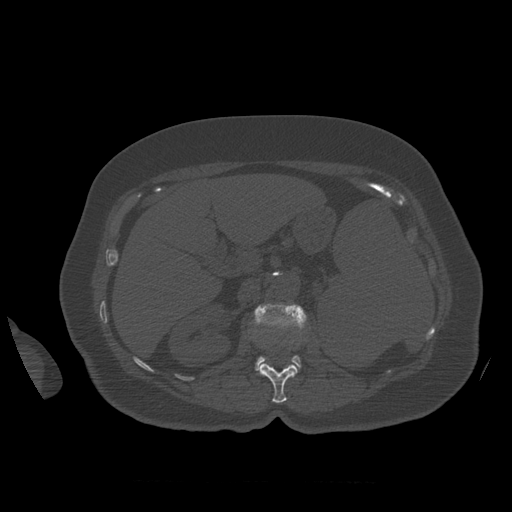
CT including the spine, one axial slice. Position 268 of 399 along the scan axis. Reconstruction kernel STANDARD. Bone window (W 1800 / L 400 HU). 1.25 mm slice thickness. 512 × 512 image matrix. Patient age 81 years. Case-level facts recorded for this patient, not image findings: primary cancer: renal; vertebrae with lytic lesions (as recorded): L1.
Outlined on this slice (semi-automatically segmented with operator editing):
- L1 vertebra: bounding box (x1, y1, x2, y2) in pixels: (261, 363, 298, 403)
- L2 vertebra: (255, 303, 307, 375)